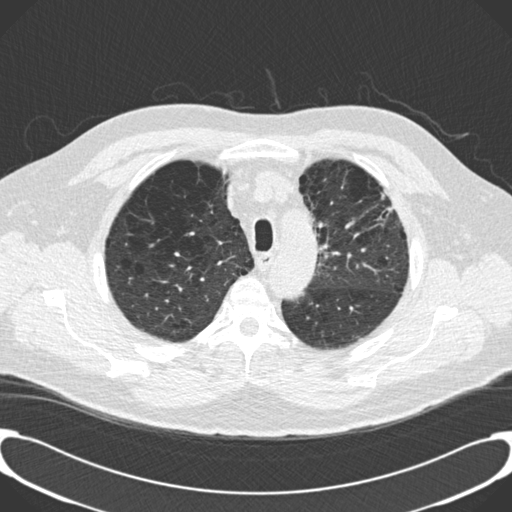
Chest CT (low-dose screening protocol), one axial image; third screening round (two years after baseline); lung window (W 1500 / L -600 HU); standard (soft-tissue) reconstruction kernel (B30f). Male, age 59 years at enrolment.
- Lesion marked by an expert reader, bounding box <363,179,408,231> (left, top, right, bottom; pixels).
- No non-calcified nodule or mass ≥4 mm was recorded by the screening reader at this exam.
- Official screen result: positive, other.
- Participant outcome: lung cancer diagnosed 134 days after this screen — bronchiolo-alveolar carcinoma, mixed mucinous and non-mucinous, left upper lobe, stage IA (AJCC 6th edition), 20 mm at pathology.